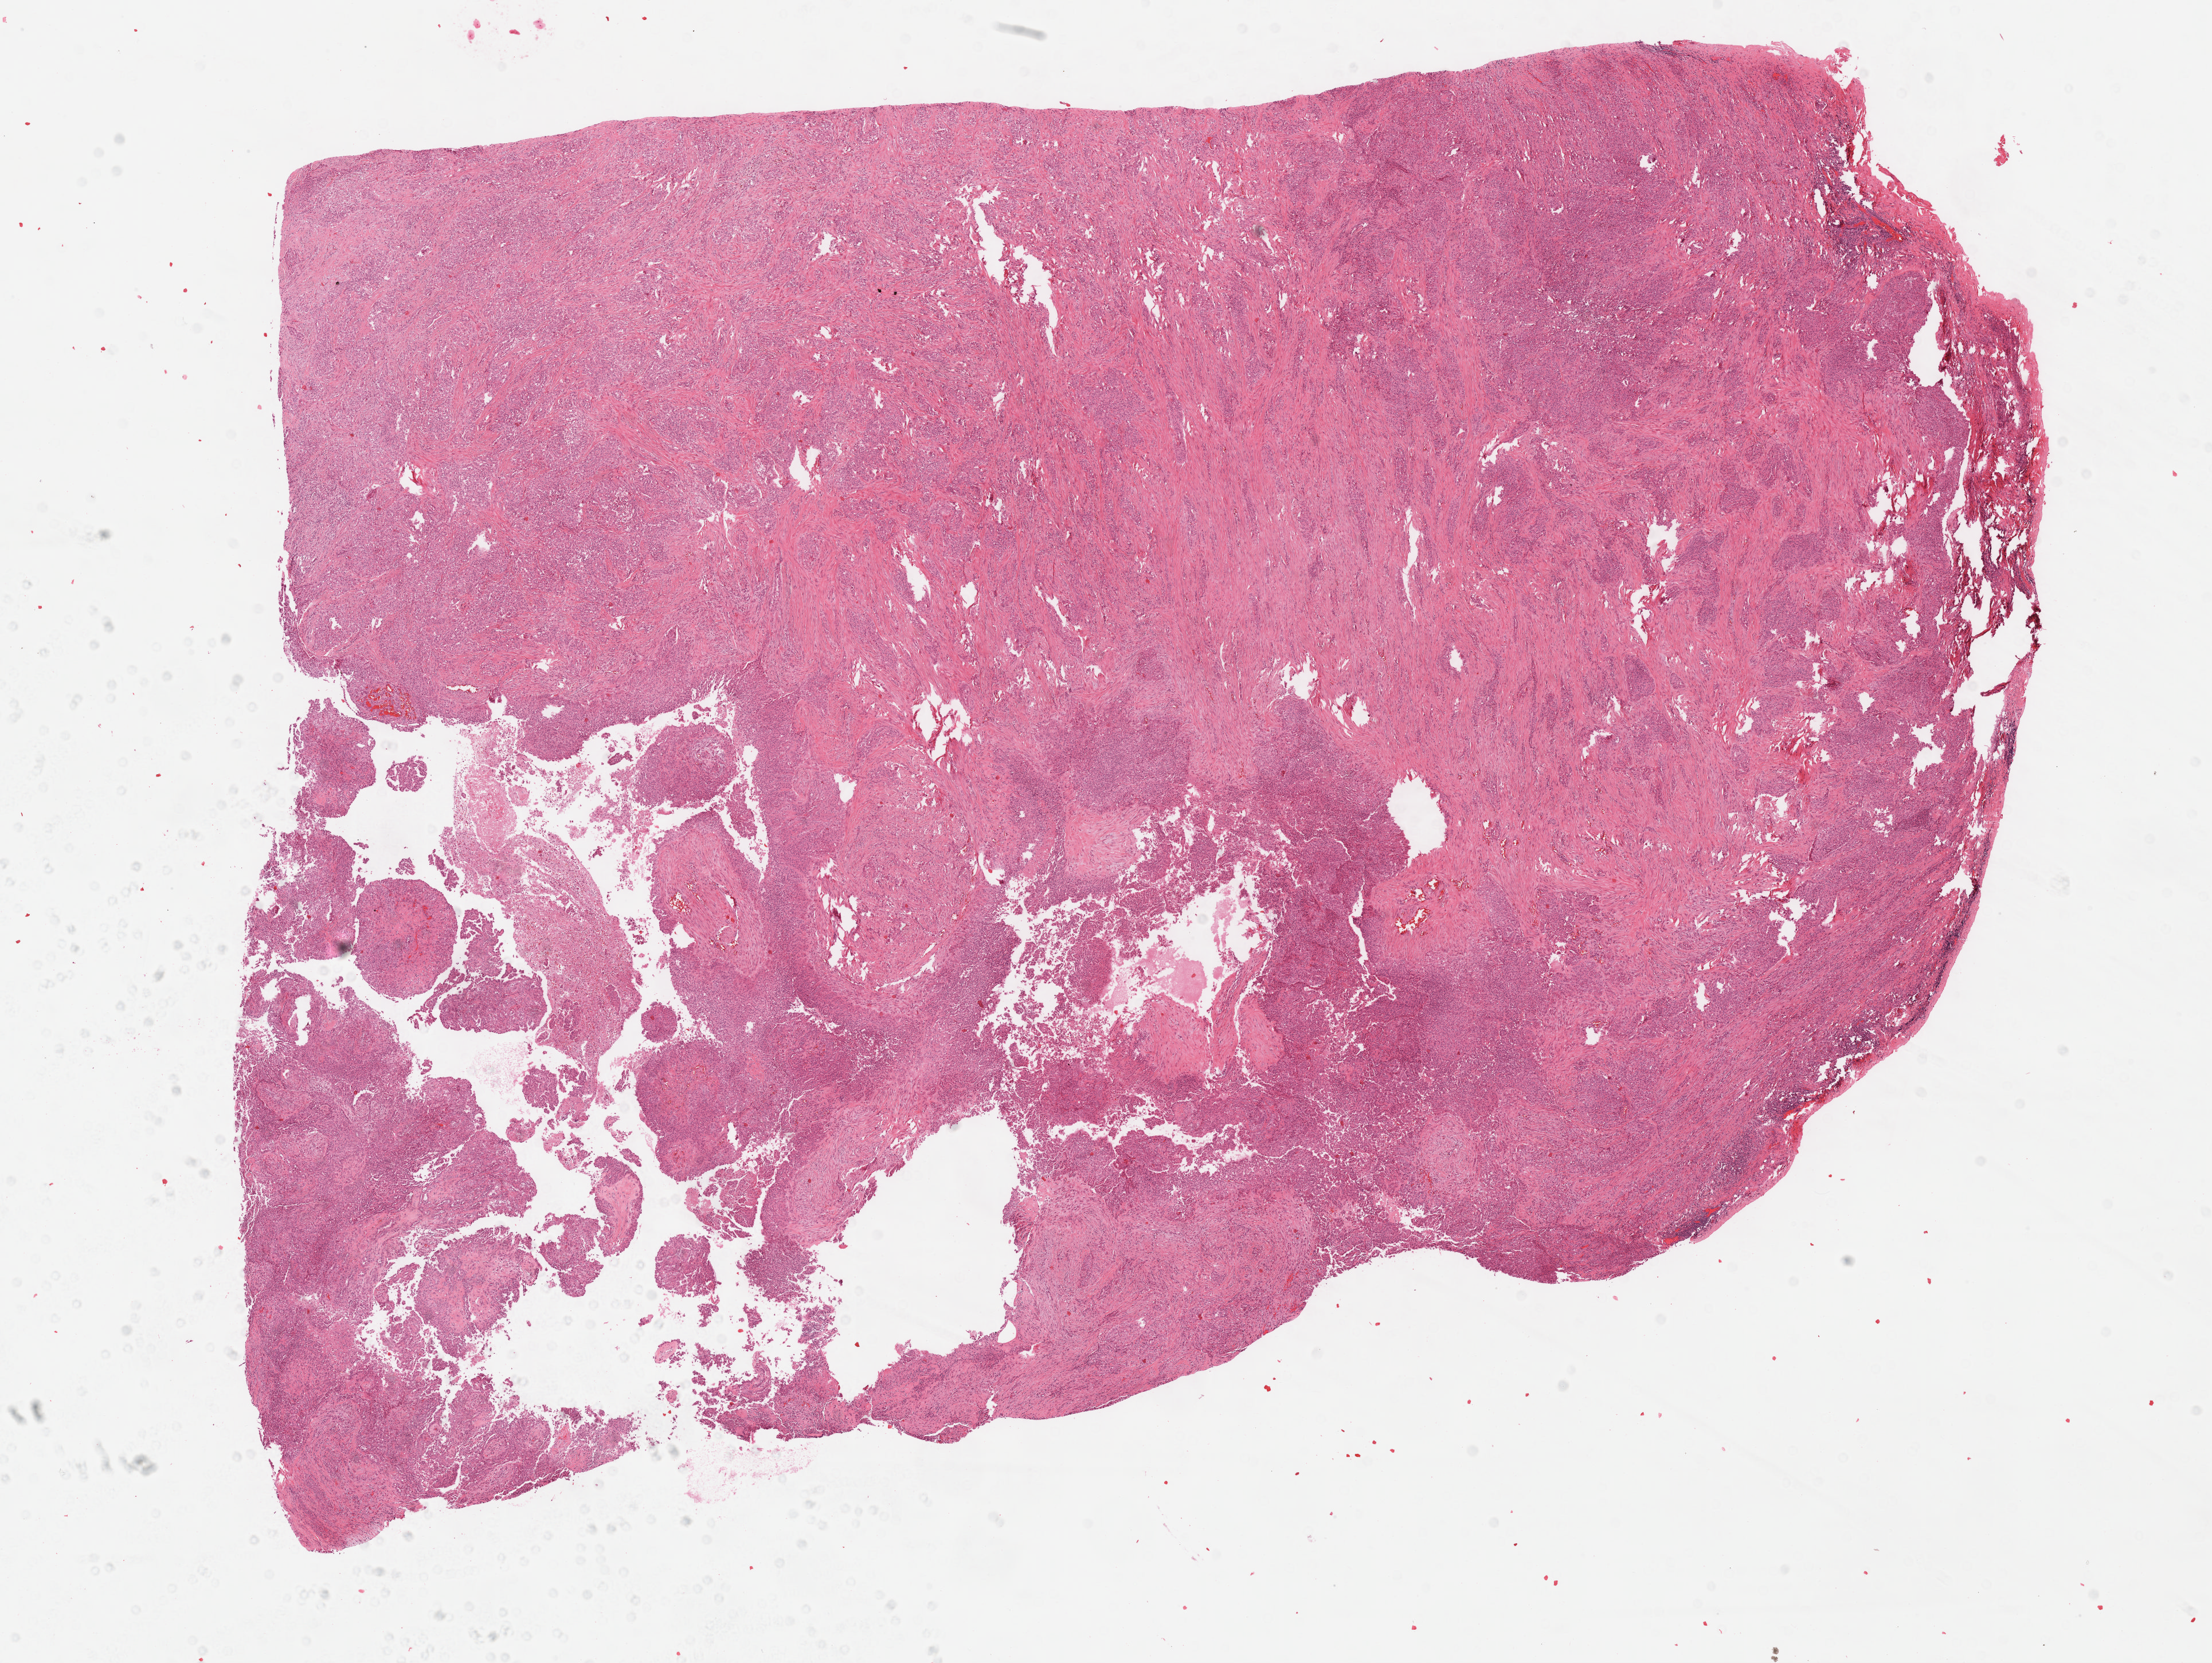
Digitized H&E tissue section (whole slide) — low-resolution overview of the scanned area, about 15.6 x 11.7 mm; formalin-fixed paraffin-embedded (FFPE) diagnostic section; primary tumour sample from the mesothelium. Patient: male, age at initial diagnosis 58 years.
AJCC pathologic stage: IV. TNM: T4 N1 MX. Histologic diagnosis: Epithelioid mesothelioma, malignant (pleura, NOS).